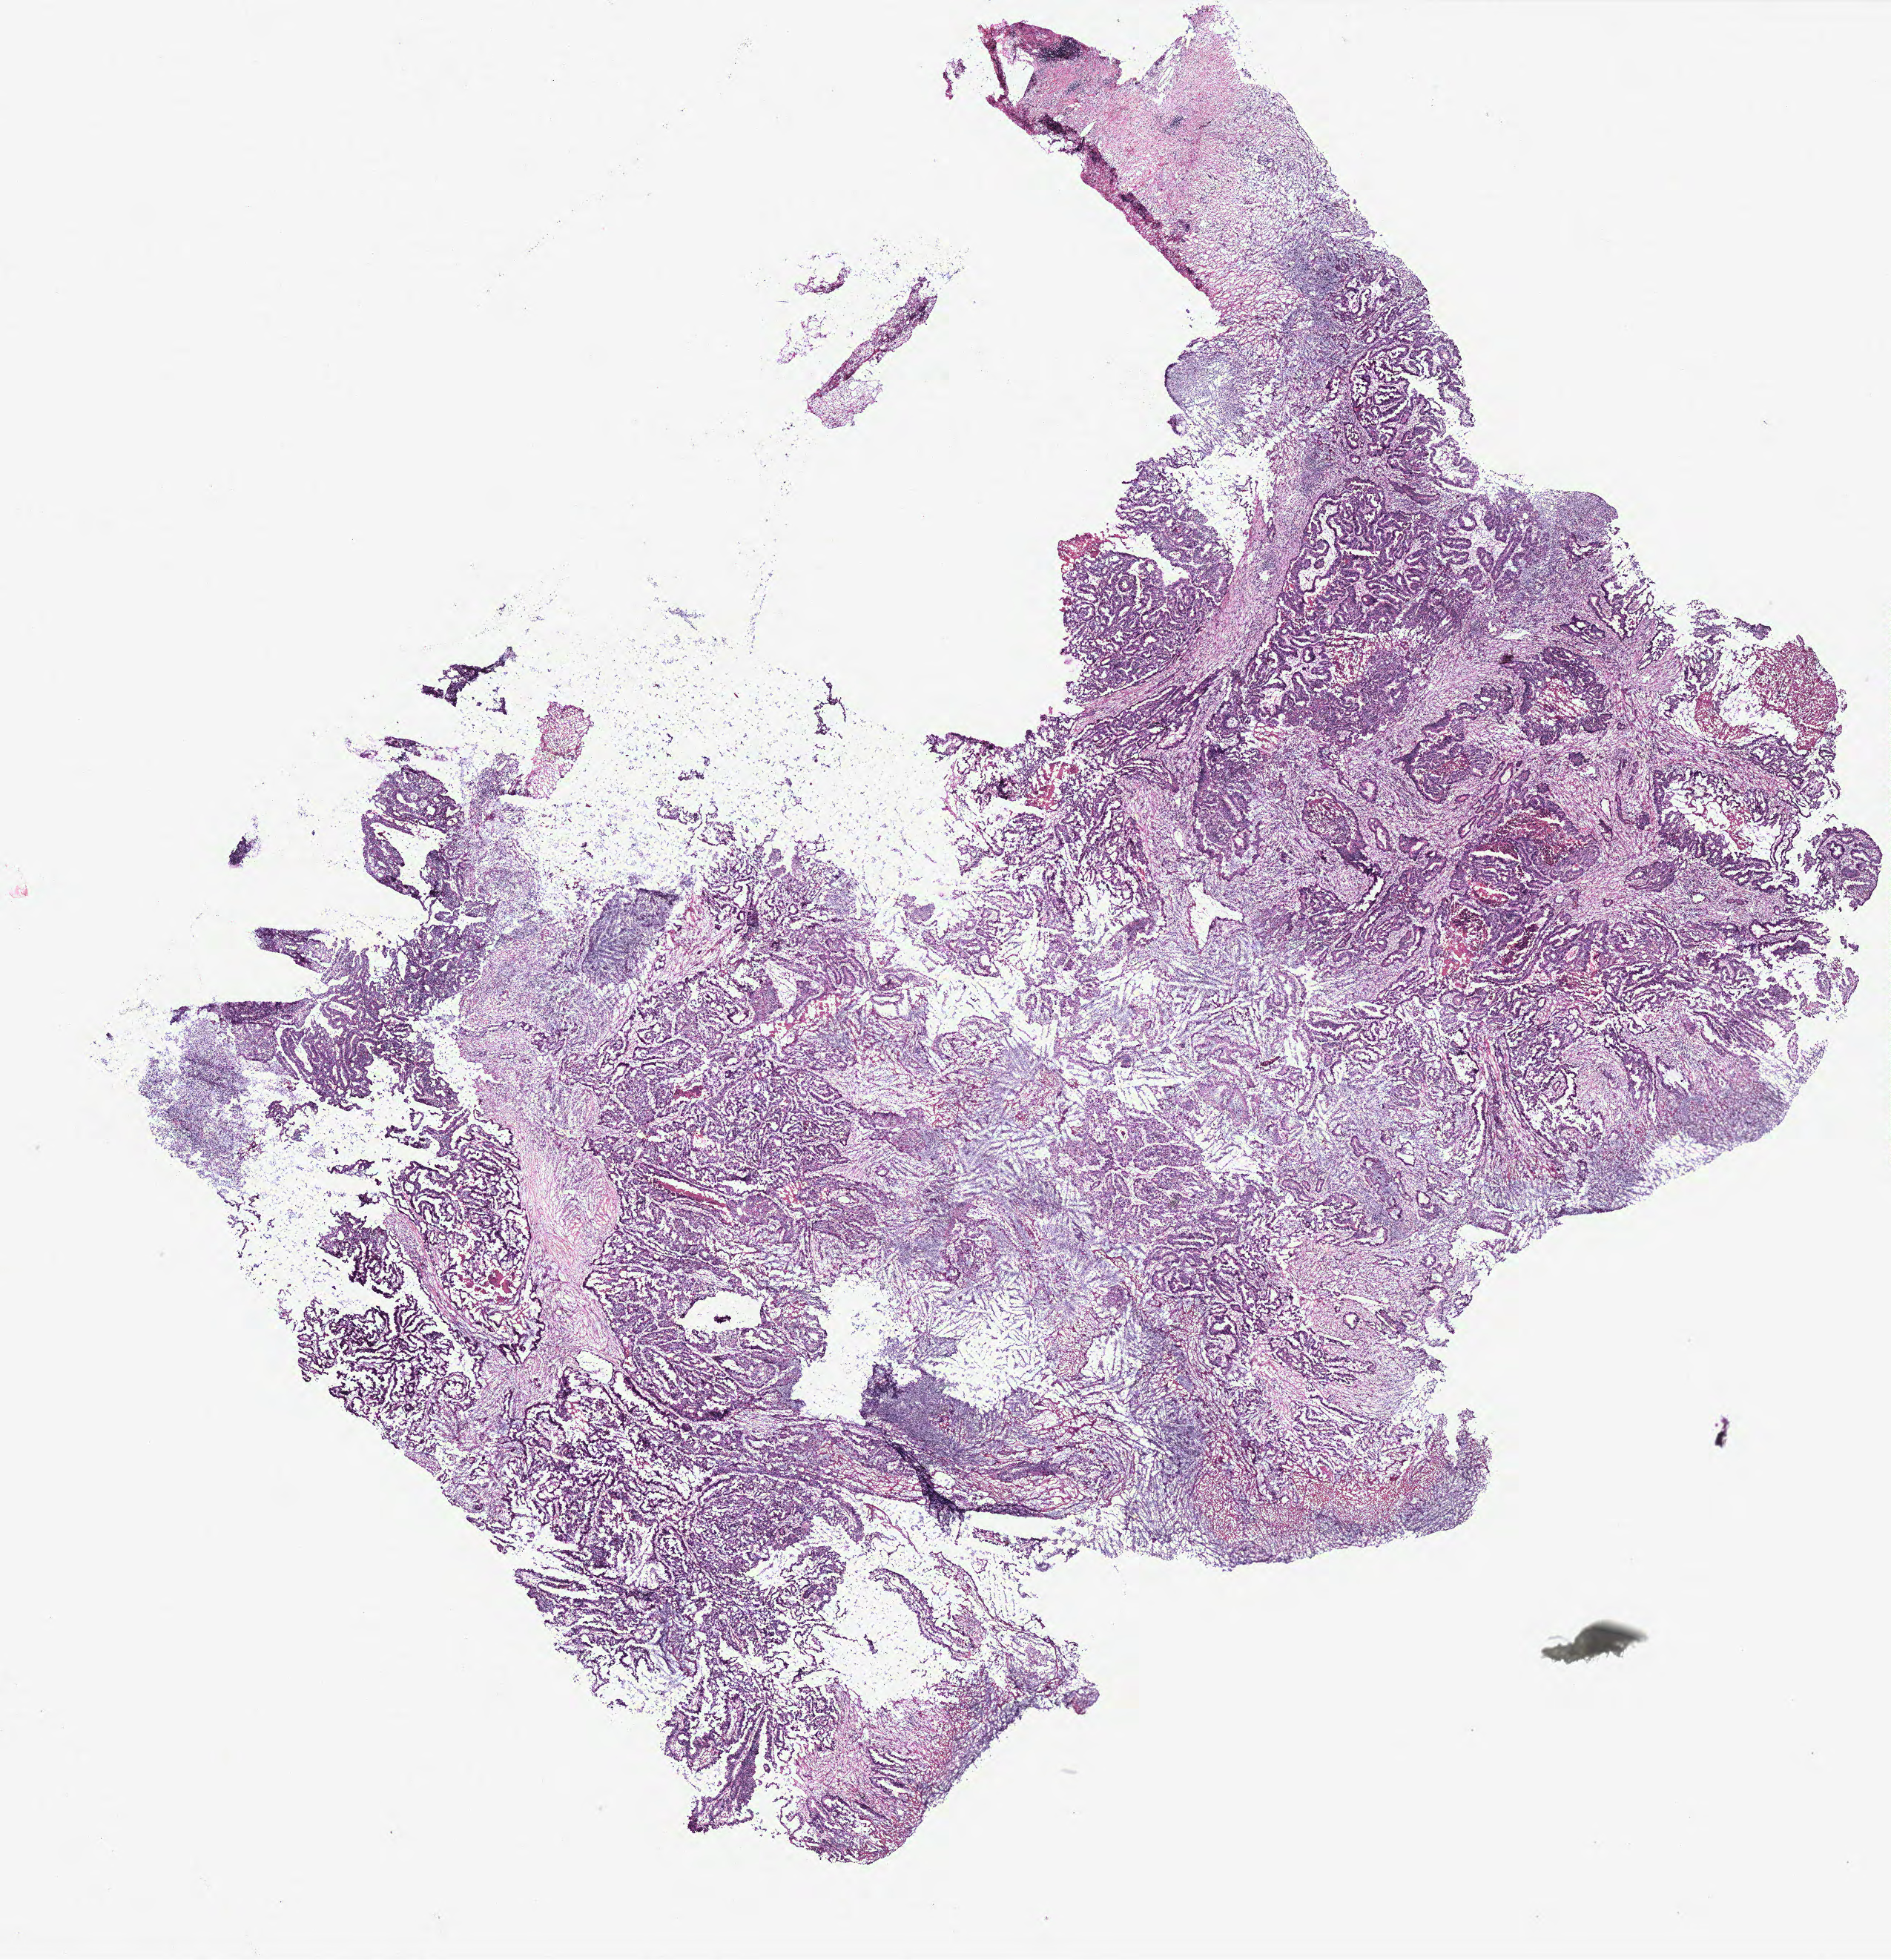
H&E whole-slide image — low-resolution overview of the scanned area, about 20.4 x 21.2 mm. Normal (non-tumour) tissue sample, colon. Patient: female, age 65 years.
• this section: normal (non-tumour) tissue from the same patient
• patient diagnosis: Adenocarcinoma, NOS